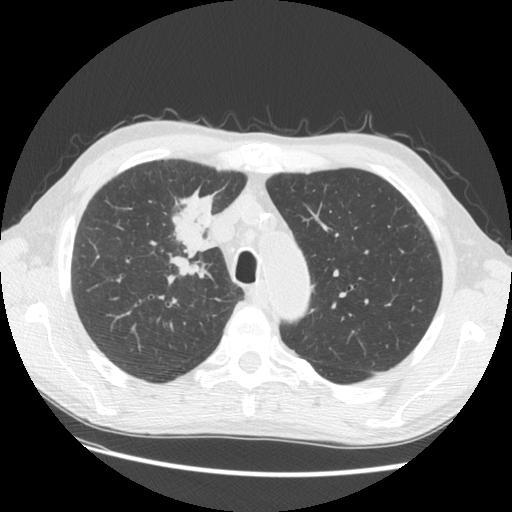
Low-dose screening chest CT, axial slice. Third screening round (two years after baseline). Lung window (W 1500 / L -600 HU). Standard (soft-tissue) reconstruction kernel (STANDARD). Slice 32 of 133 in the series. 512 × 512 image matrix. Male participant, aged 73 years at enrolment. Current smoker at enrolment.
• Lesion marked by an expert reader, bounding box <142,182,232,280> (left, top, right, bottom; pixels).
• The screening reader recorded 4 non-calcified nodules or masses ≥4 mm on this exam (right upper lobe, right upper lobe, right upper lobe, left lower lobe); which of them this box marks is not recorded.
• Official screen result: positive, other.
• Lung cancer was diagnosed 48 days after this screen: squamous cell carcinoma, NOS, right upper lobe, poorly differentiated (G3), stage IIIB (AJCC 6th edition), 56 mm at pathology.